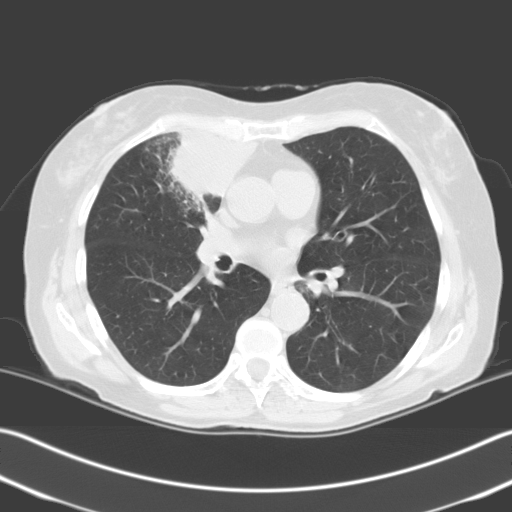
Low-dose screening chest CT, one axial slice. Slice 119 of 204 in the series (ordered by position). Lung window (W 1500 / L -600 HU). 3.2 mm slice thickness. 512 × 512 image matrix.
Outlined on this slice (outlined manually by an expert reader):
- lesion 1 (tumor, upper lobe of right lung): bounding box <169,131,256,207> (left, top, right, bottom; pixels)